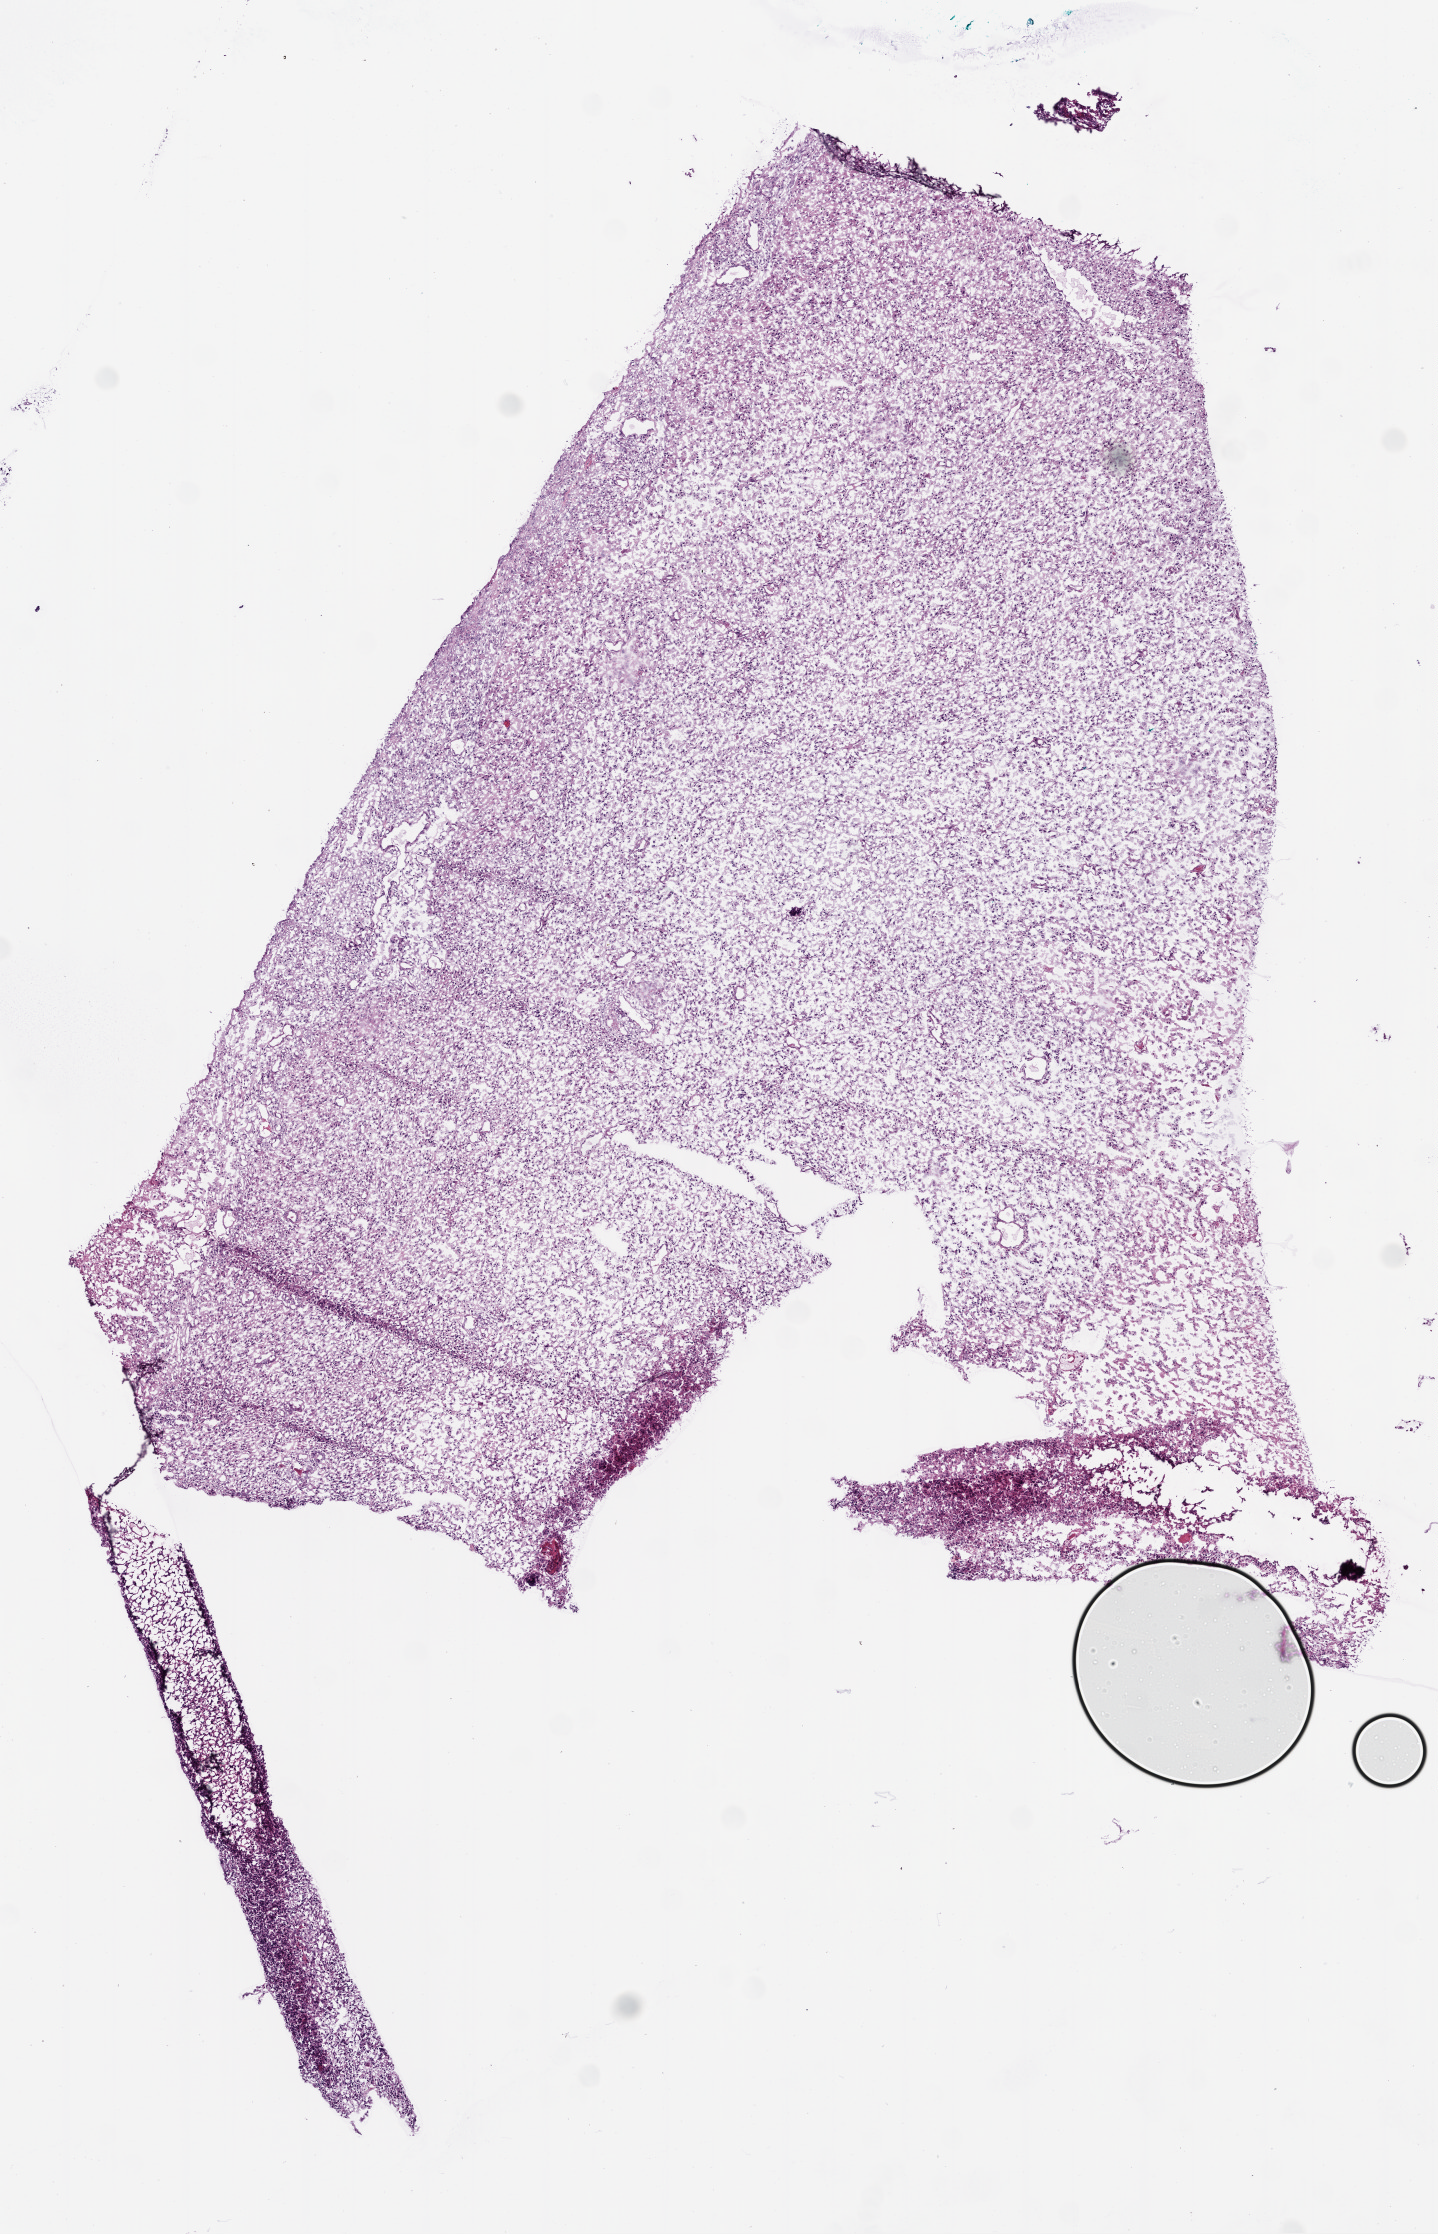
Whole-slide histology image, Hematoxylin and eosin (H&E) stained — whole scanned area (about 5.8 x 9.0 mm, acquisition: 20x scan) shown as a low-resolution overview, frozen section from the bottom of the tissue portion, primary tumour sample from the brain. Patient: female, age at initial diagnosis 70 years. Pathologist review of this section (percent, as recorded): tumour cells 100%, tumour nuclei 80%, normal cells 0%, stromal cells 0%, necrosis 0%. Inflammatory infiltration, as recorded: lymphocyte infiltration 0%, neutrophil infiltration 0%.
Diagnosis: Glioblastoma.